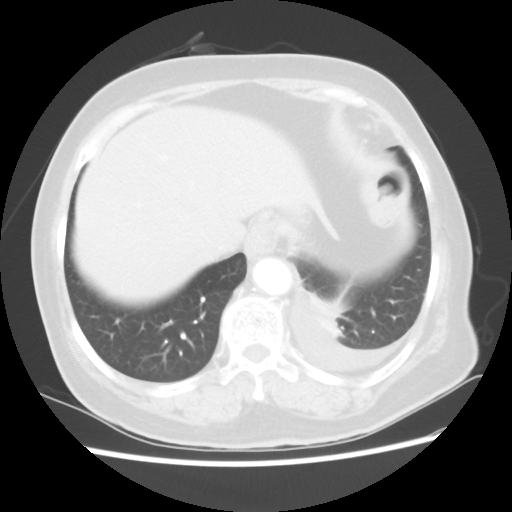
Chest CT, one axial slice; position 5 of 80 along the scan axis; lung window (W 1500 / L -600 HU); 512 × 512 image matrix, field of view 343 × 343 mm. Patient: female, 68 years. Case-level facts recorded for this patient, not image findings: clinical TNM (as recorded): T1c N0 M1.
Structures marked on this image (rectangle marked by the reading radiologist):
- lung tumour (recorded histology: adenocarcinoma): bounding box [x1, y1, x2, y2] px = [307, 288, 355, 343]